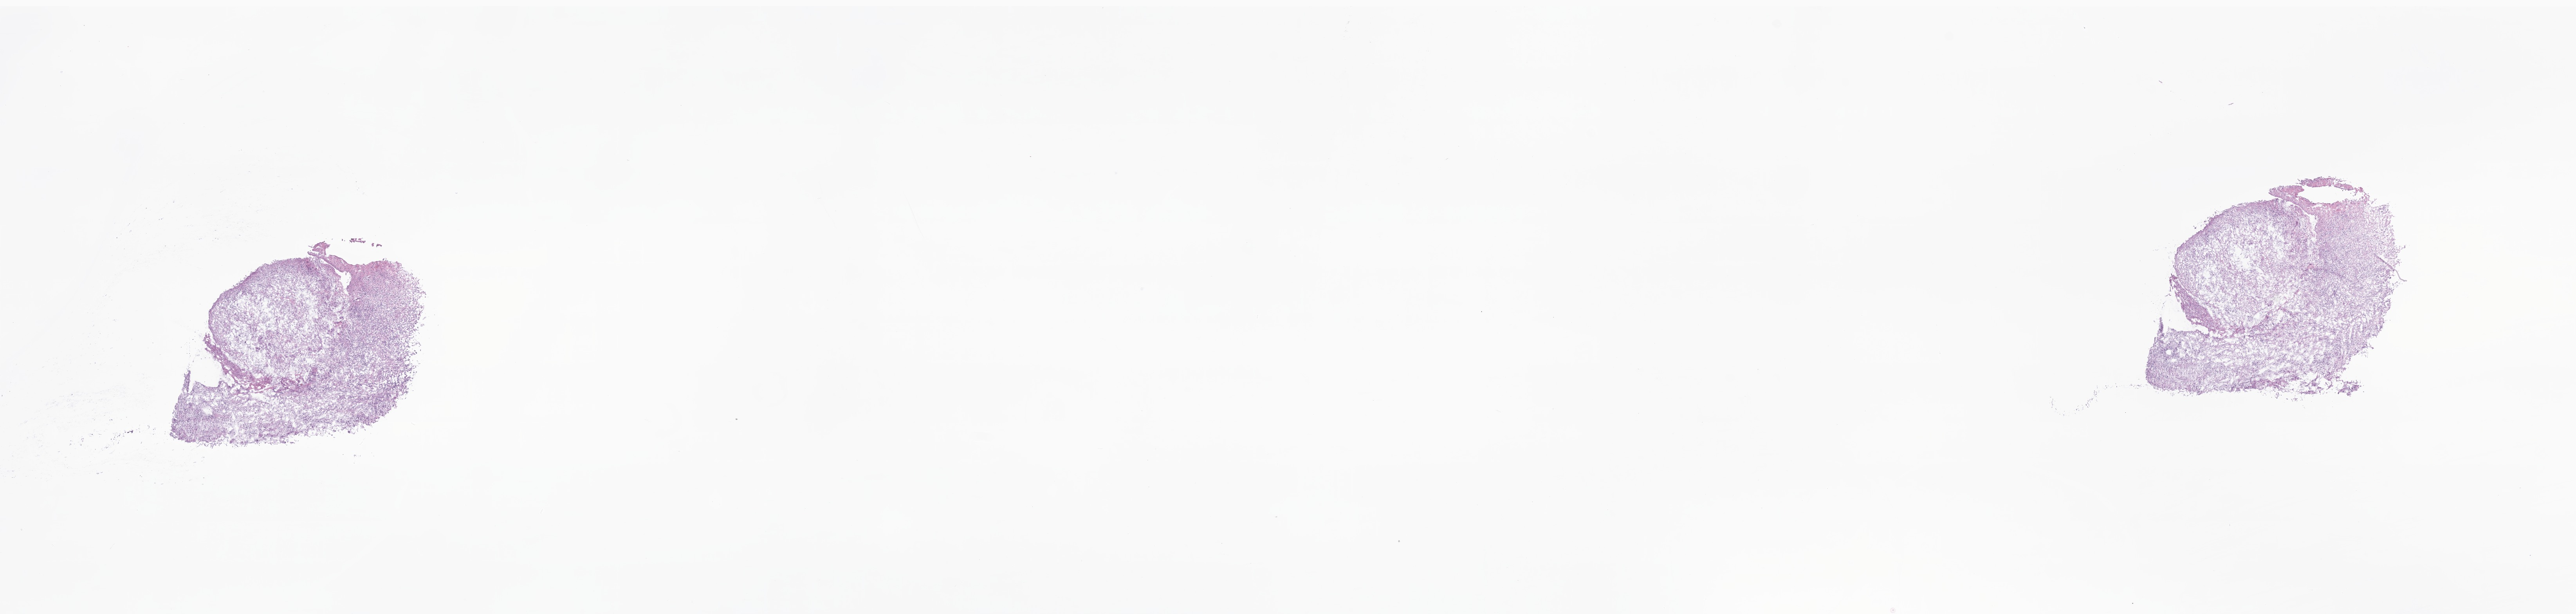
H&E whole-slide image of tumor tissue from the brain, low-resolution overview of the scanned area, about 27.7 x 6.6 mm; frozen section (OCT-embedded). Patient female; age 269 days.
* recorded diagnosis: Glioma, malignant